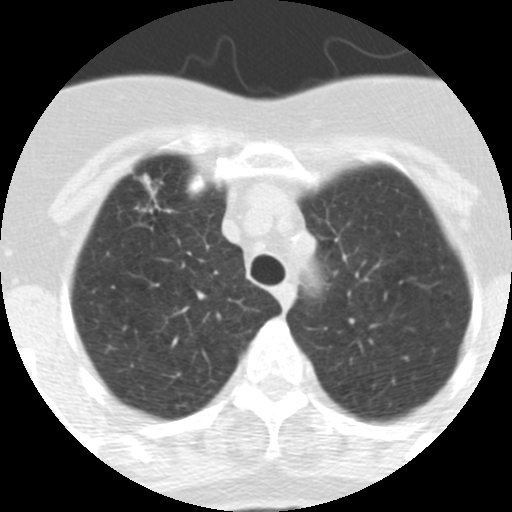
Low-dose screening chest CT, one axial slice; position 252 of 313 along the scan axis; reconstruction kernel STANDARD; 120 kVp; lung window (W 1500 / L -600 HU); 2.5 mm slice thickness; 512 × 512 image matrix, field of view 253 × 253 mm.
Annotated regions visible in this slice (outlined manually by an expert reader):
- lesion 1 (tumor, upper lobe of right lung): bounding box (x1, y1, x2, y2) in pixels: (139, 173, 157, 197)